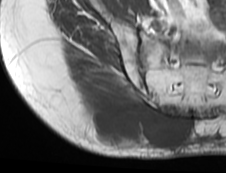
MRI of an extremity soft-tissue mass, one axial slice. Position 49 of 73 along the scan axis. MR volume resampled by the dataset authors to the PET/CT grid (not the native acquisition matrix). 3.27 mm slice thickness. 226 × 173 image matrix. Female patient. From the clinical record (not read from this slice): histological type: spindle cell suggestive of myxofibrosarcoma; grade: intermediate; site of the primary tumour: right buttock.
Structures marked on this image (expert contour drawn on MRI and transferred to this co-registered scan by the dataset authors):
- gross tumour volume (mass): bounding box [x1, y1, x2, y2] px = [77, 90, 190, 150]